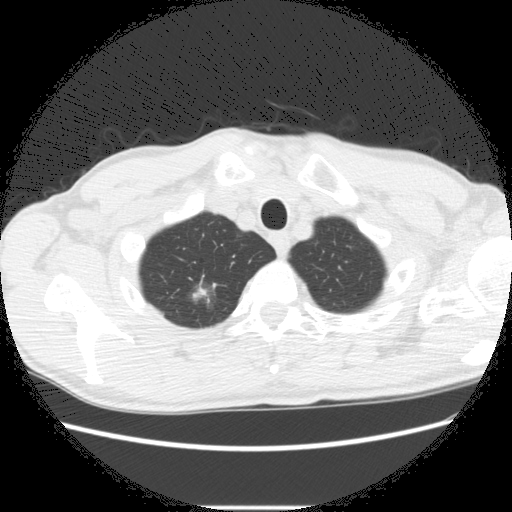
Low-dose screening chest CT, one axial slice; position 256 of 282 along the scan axis; reconstruction kernel STANDARD; 120 kVp; lung window (W 1500 / L -600 HU); 2.5 mm slice thickness; 512 × 512 image matrix.
Outlined on this slice (manually delineated by an expert):
- lesion 2 (nodule, upper lobe of right lung): bounding box [x1, y1, x2, y2] px = [191, 283, 211, 302]